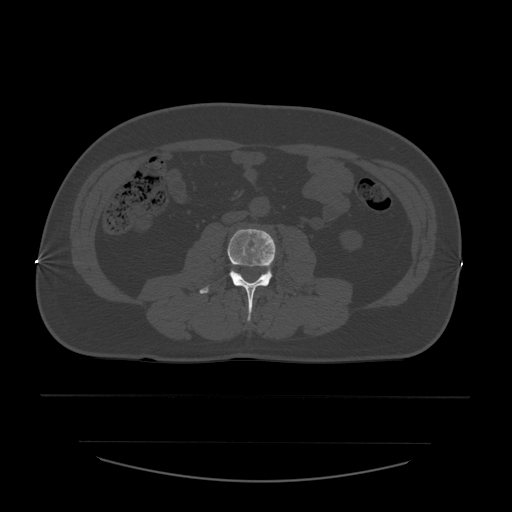
CT including the spine, one axial slice. Position 172 of 532 along the scan axis. Bone window (W 1800 / L 400 HU). 512 × 512 image matrix. Patient age 44 years. Case-level facts recorded for this patient, not image findings: primary cancer: soft tissue sarcoma.
Outlined on this slice (semi-automatically segmented with operator editing):
- L3 vertebra: bounding box (x1, y1, x2, y2) in pixels: (200, 229, 276, 321)